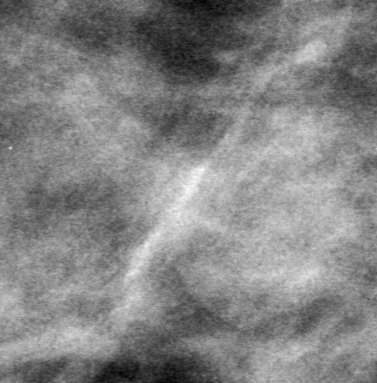
Cropped region of a digitized screen-film mammogram centred on a radiologist-marked abnormality; right breast; MLO view.
- Finding: mass, shape oval, margins obscured; BI-RADS assessment category 0 (incomplete: needs additional imaging); subtlety rating 3 on a 1 (subtle) to 5 (obvious) scale; pathology result (as recorded, not read from the image): benign.